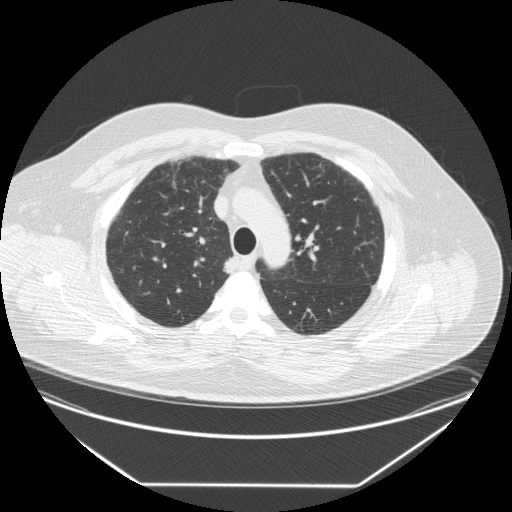
Low-dose screening chest CT, one axial slice. Lung window (W 1500 / L -600 HU). 2.5 mm slice thickness. 512 × 512 image matrix, field of view 440 × 440 mm.
Annotated regions visible in this slice (manually delineated by an expert):
- lesion 1 (tumor, upper lobe of right lung): bounding box [x1, y1, x2, y2] px = [224, 255, 237, 274]